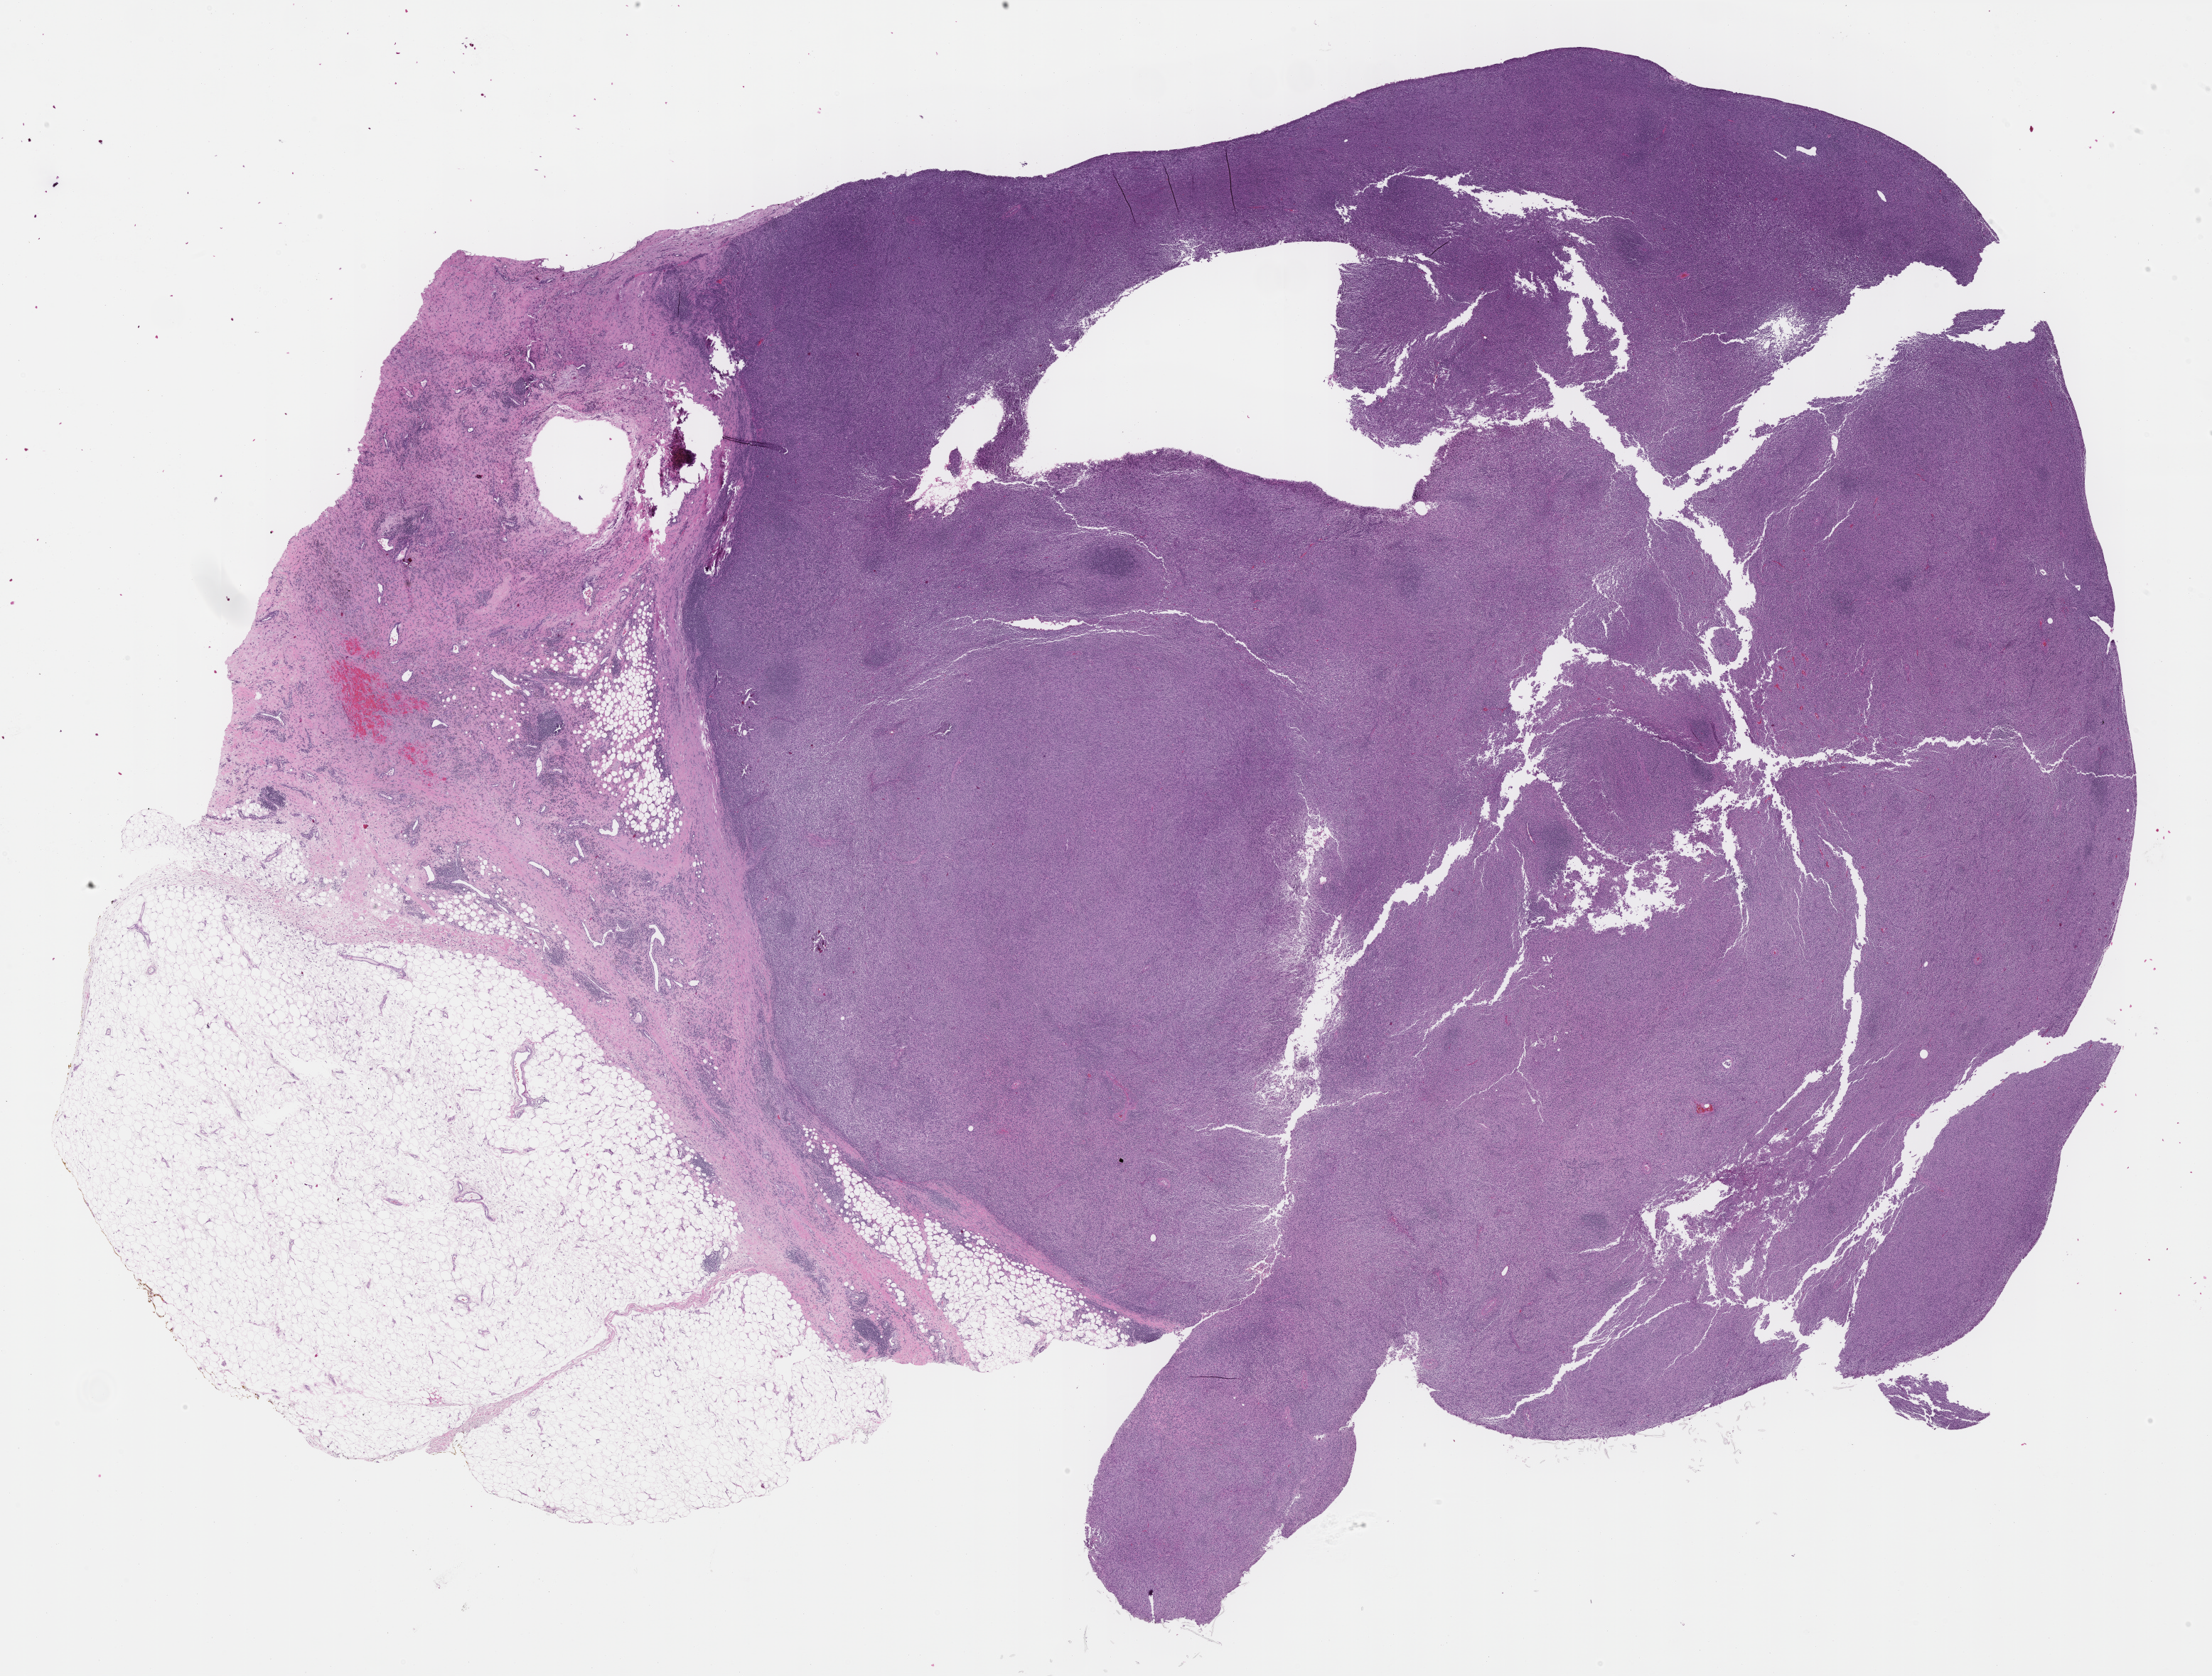
Whole-slide histology image, H&E-stained — a low-resolution overview of the entire scanned area, about 25.0 x 19.0 mm; FFPE section; primary tumour sample from the connective, subcutaneous and other soft tissues. Male, age 63 years at initial diagnosis.
Diagnosis: Malignant fibrous histiocytoma.